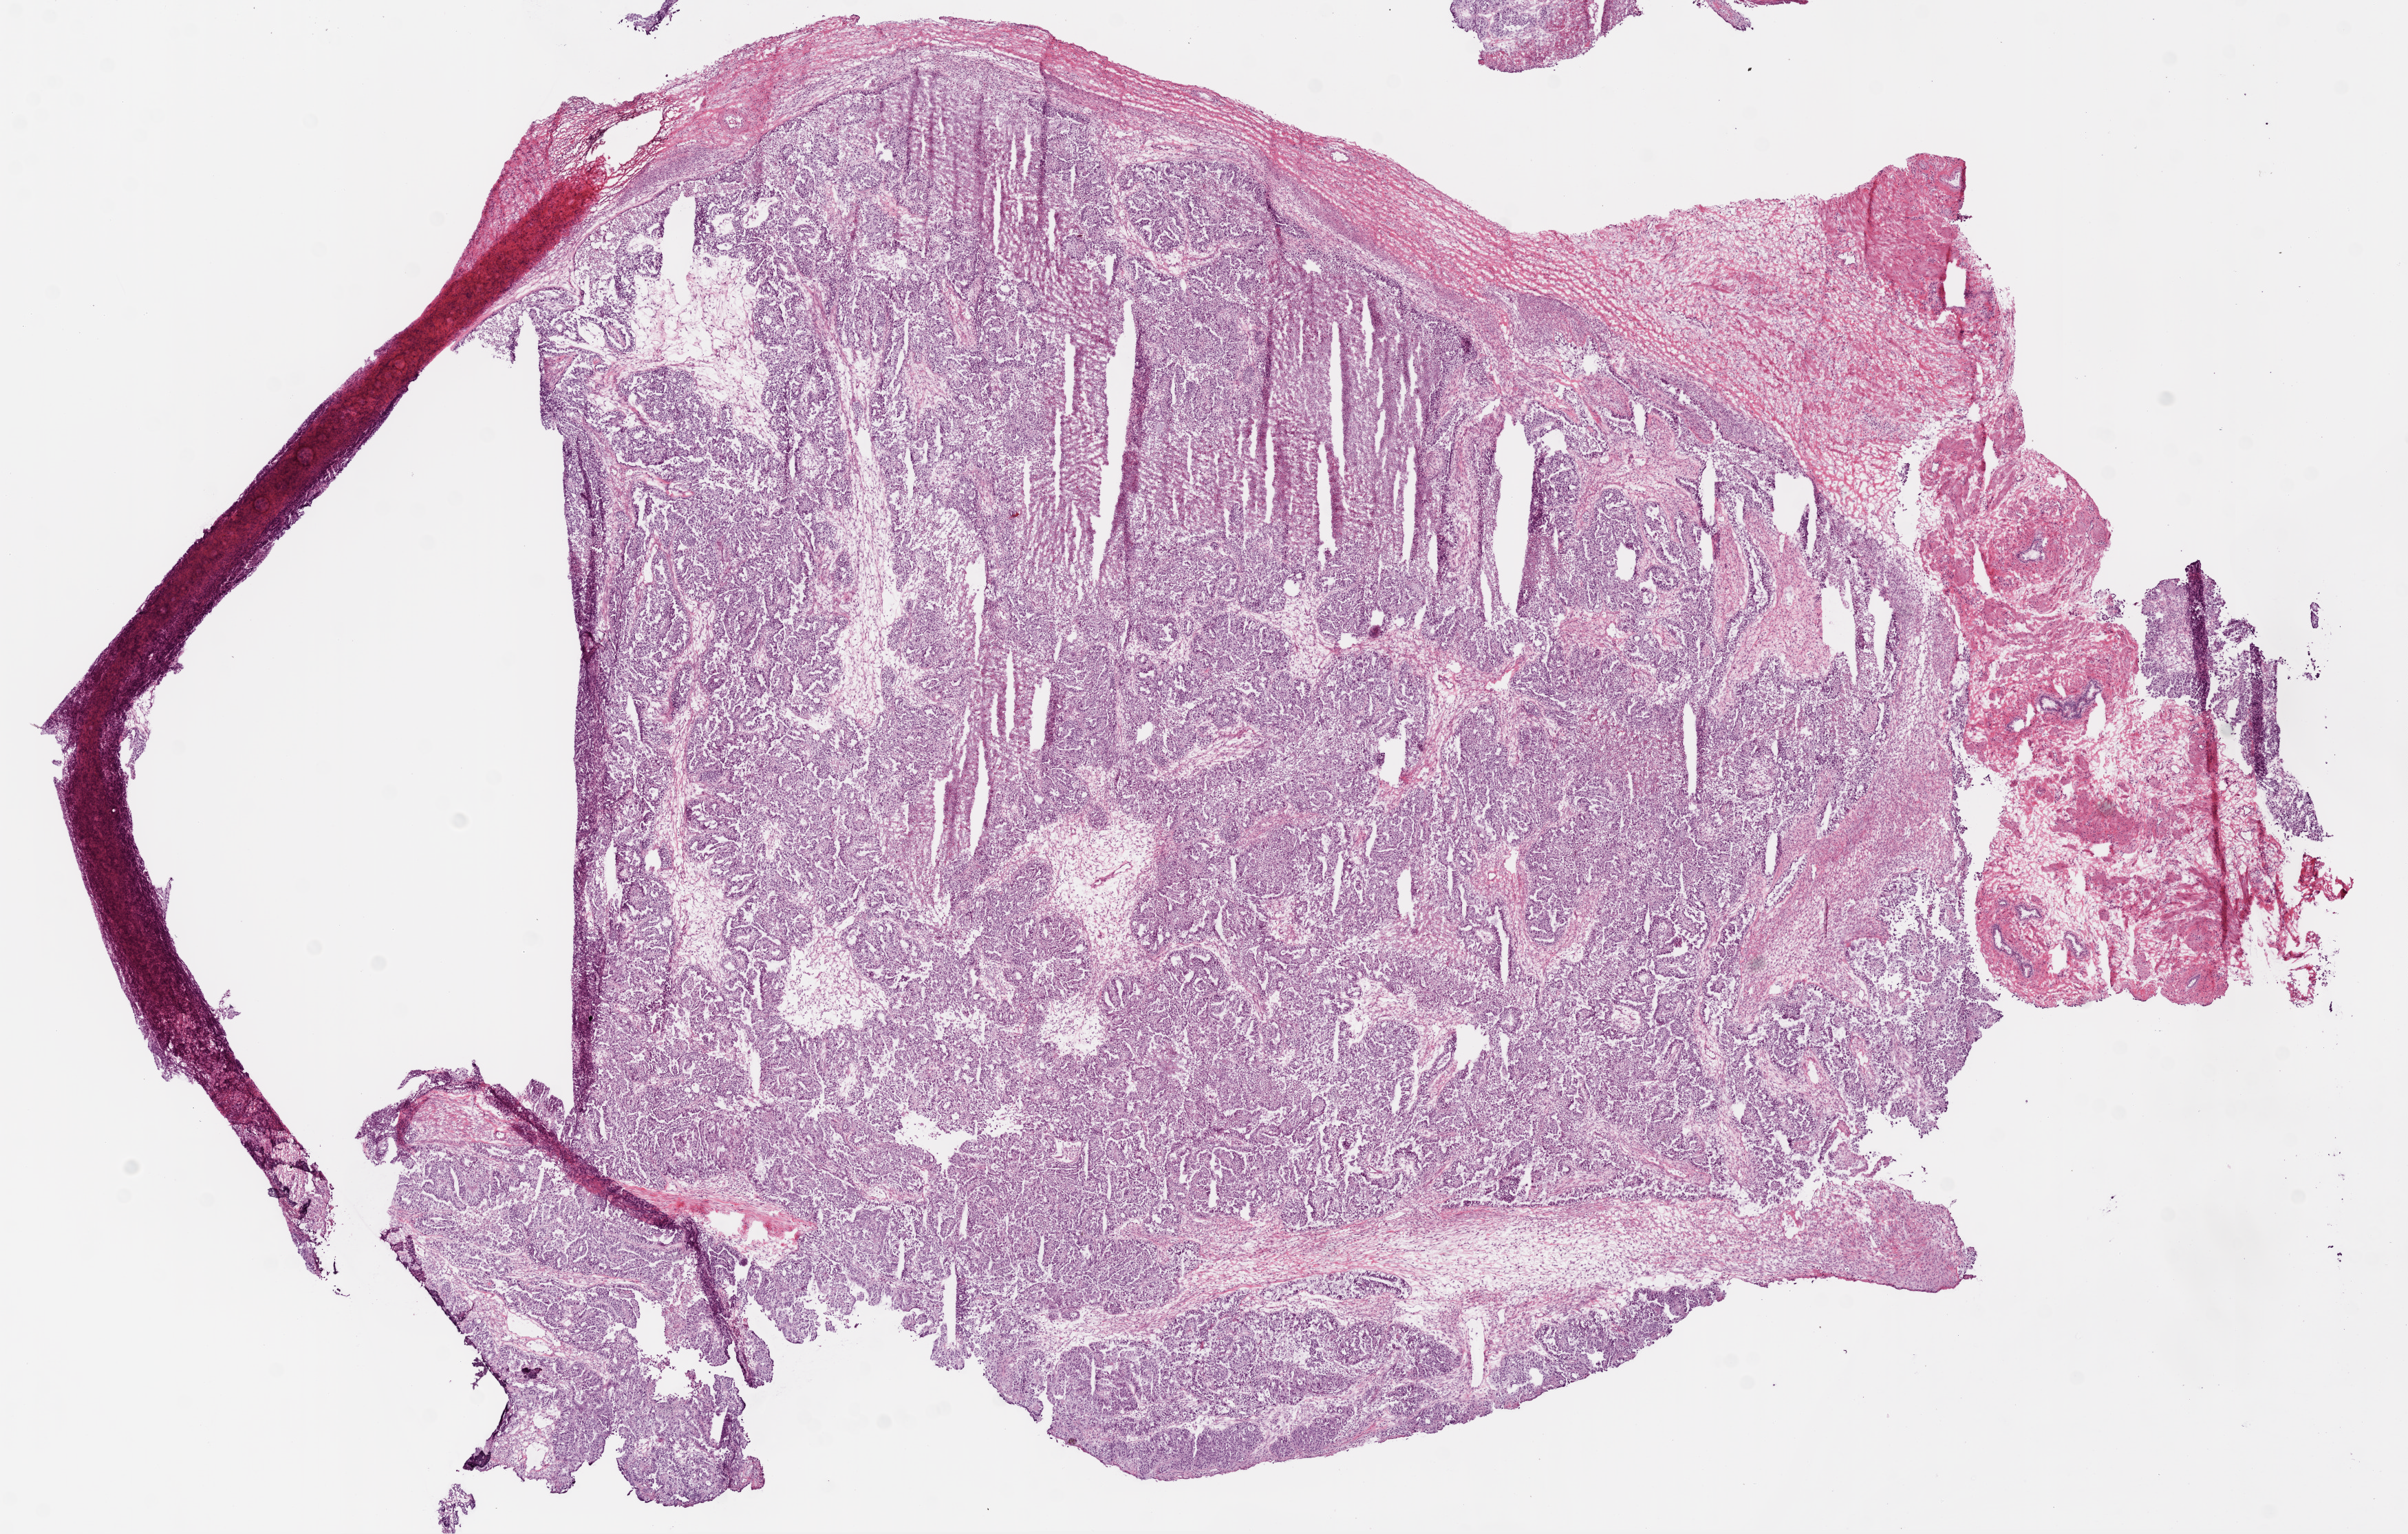
Digitized H&E-stained tissue section (whole slide) — low-resolution overview of the scanned area, about 14.0 x 8.9 mm, frozen section from the bottom of the tissue portion, ovary, primary tumour sample. Patient: female, age at initial diagnosis 73 years. Histologic grade: G3 (poorly differentiated). Slide review estimates, as recorded: tumour cells 85%, tumour nuclei 90%, normal cells 0%, stromal cells 10%, necrosis 5%.
• laterality: bilateral
• FIGO stage: IIIC
• diagnosis: Serous cystadenocarcinoma, NOS